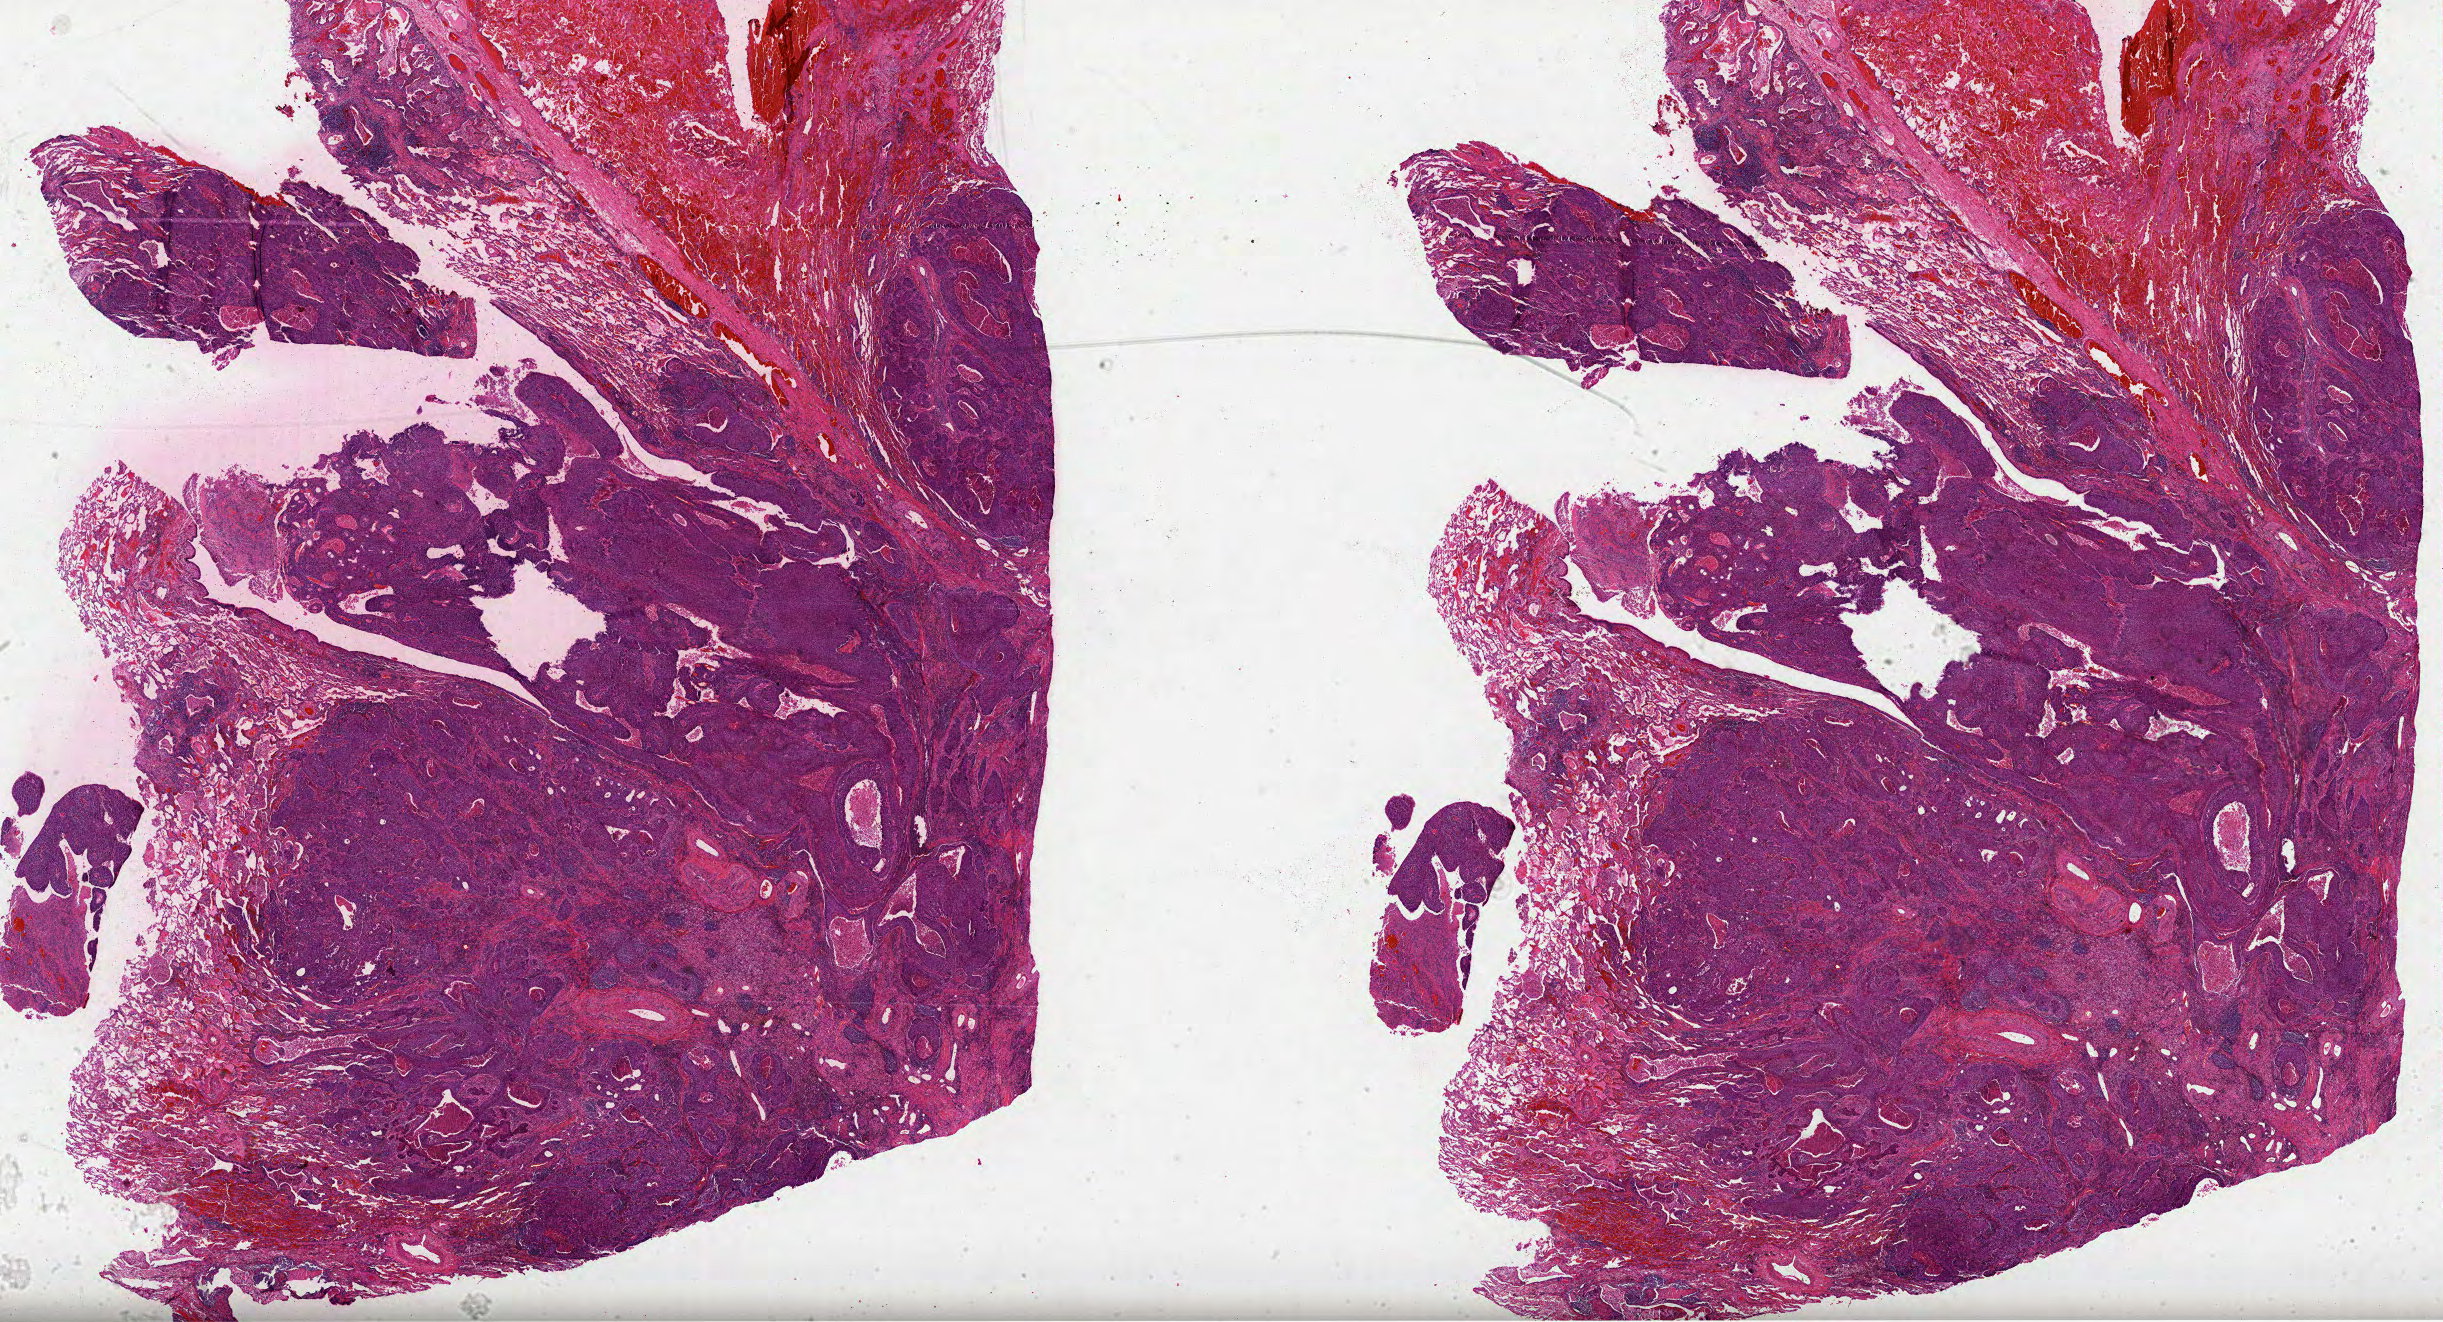
H&E-stained whole-slide image, low-resolution overview of the scanned area, about 39.4 x 21.3 mm (slide scanned at 40x), formalin-fixed paraffin-embedded (FFPE) diagnostic section, lung, primary tumour sample. Male patient; age at initial diagnosis 66 years.
- pathologic diagnosis: Squamous cell carcinoma, NOS (upper lobe, lung)
- AJCC pathologic stage: IIIA (6th edition)
- laterality: left